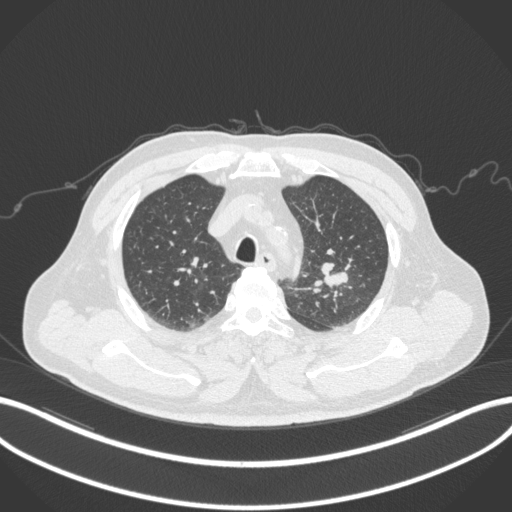
Chest CT, one axial slice. Position 237 of 286 along the scan axis. Reconstruction kernel B31f. 120 kVp. Lung window (W 1500 / L -600 HU). 512 × 512 image matrix, field of view 400 × 400 mm. Patient: male, 67 years. From the clinical record (not read from this slice): clinical TNM (as recorded): T2a N1 M0.
Structures marked on this image (bounding box drawn by a radiologist):
- lung tumour (recorded histology: adenocarcinoma): bounding box (x1, y1, x2, y2) in pixels: (319, 257, 351, 290)